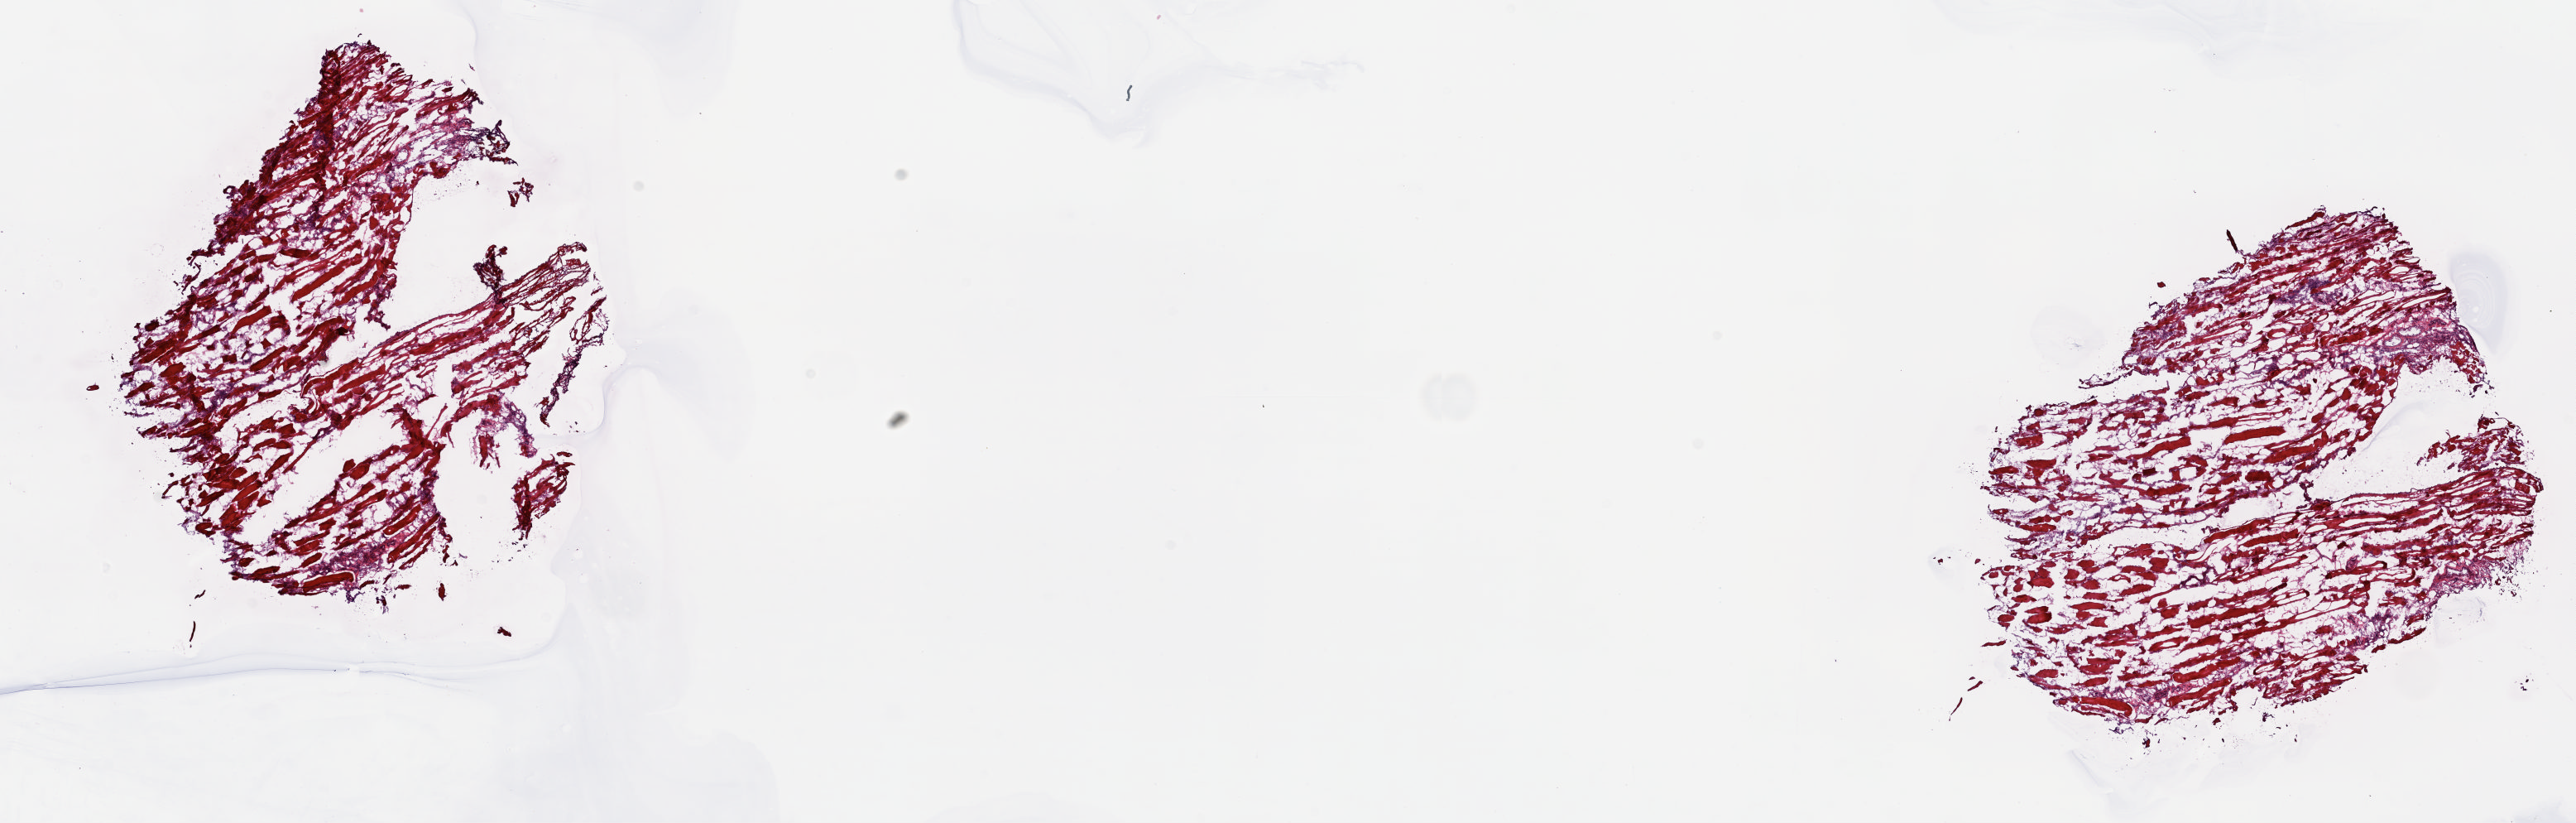
Whole-slide histology image, Hematoxylin and eosin (H&E) stained — low-resolution overview of the scanned area, about 25.1 x 8.0 mm; frozen section from the top of the tissue portion; mesothelium, solid tissue normal (non-tumour tissue) sample. Male, age 60 years at initial diagnosis. Slide review estimates, as recorded: tumour cells 0%, tumour nuclei 0%, normal cells 1%, stromal cells 99%, necrosis 0%. Infiltration values recorded for this section: lymphocyte infiltration 5%, monocyte infiltration 0%, neutrophil infiltration 0%.
This section: solid tissue normal (non-tumour) sample from the same patient. Patient diagnosis: Mesothelioma, biphasic, malignant (pleura, NOS).